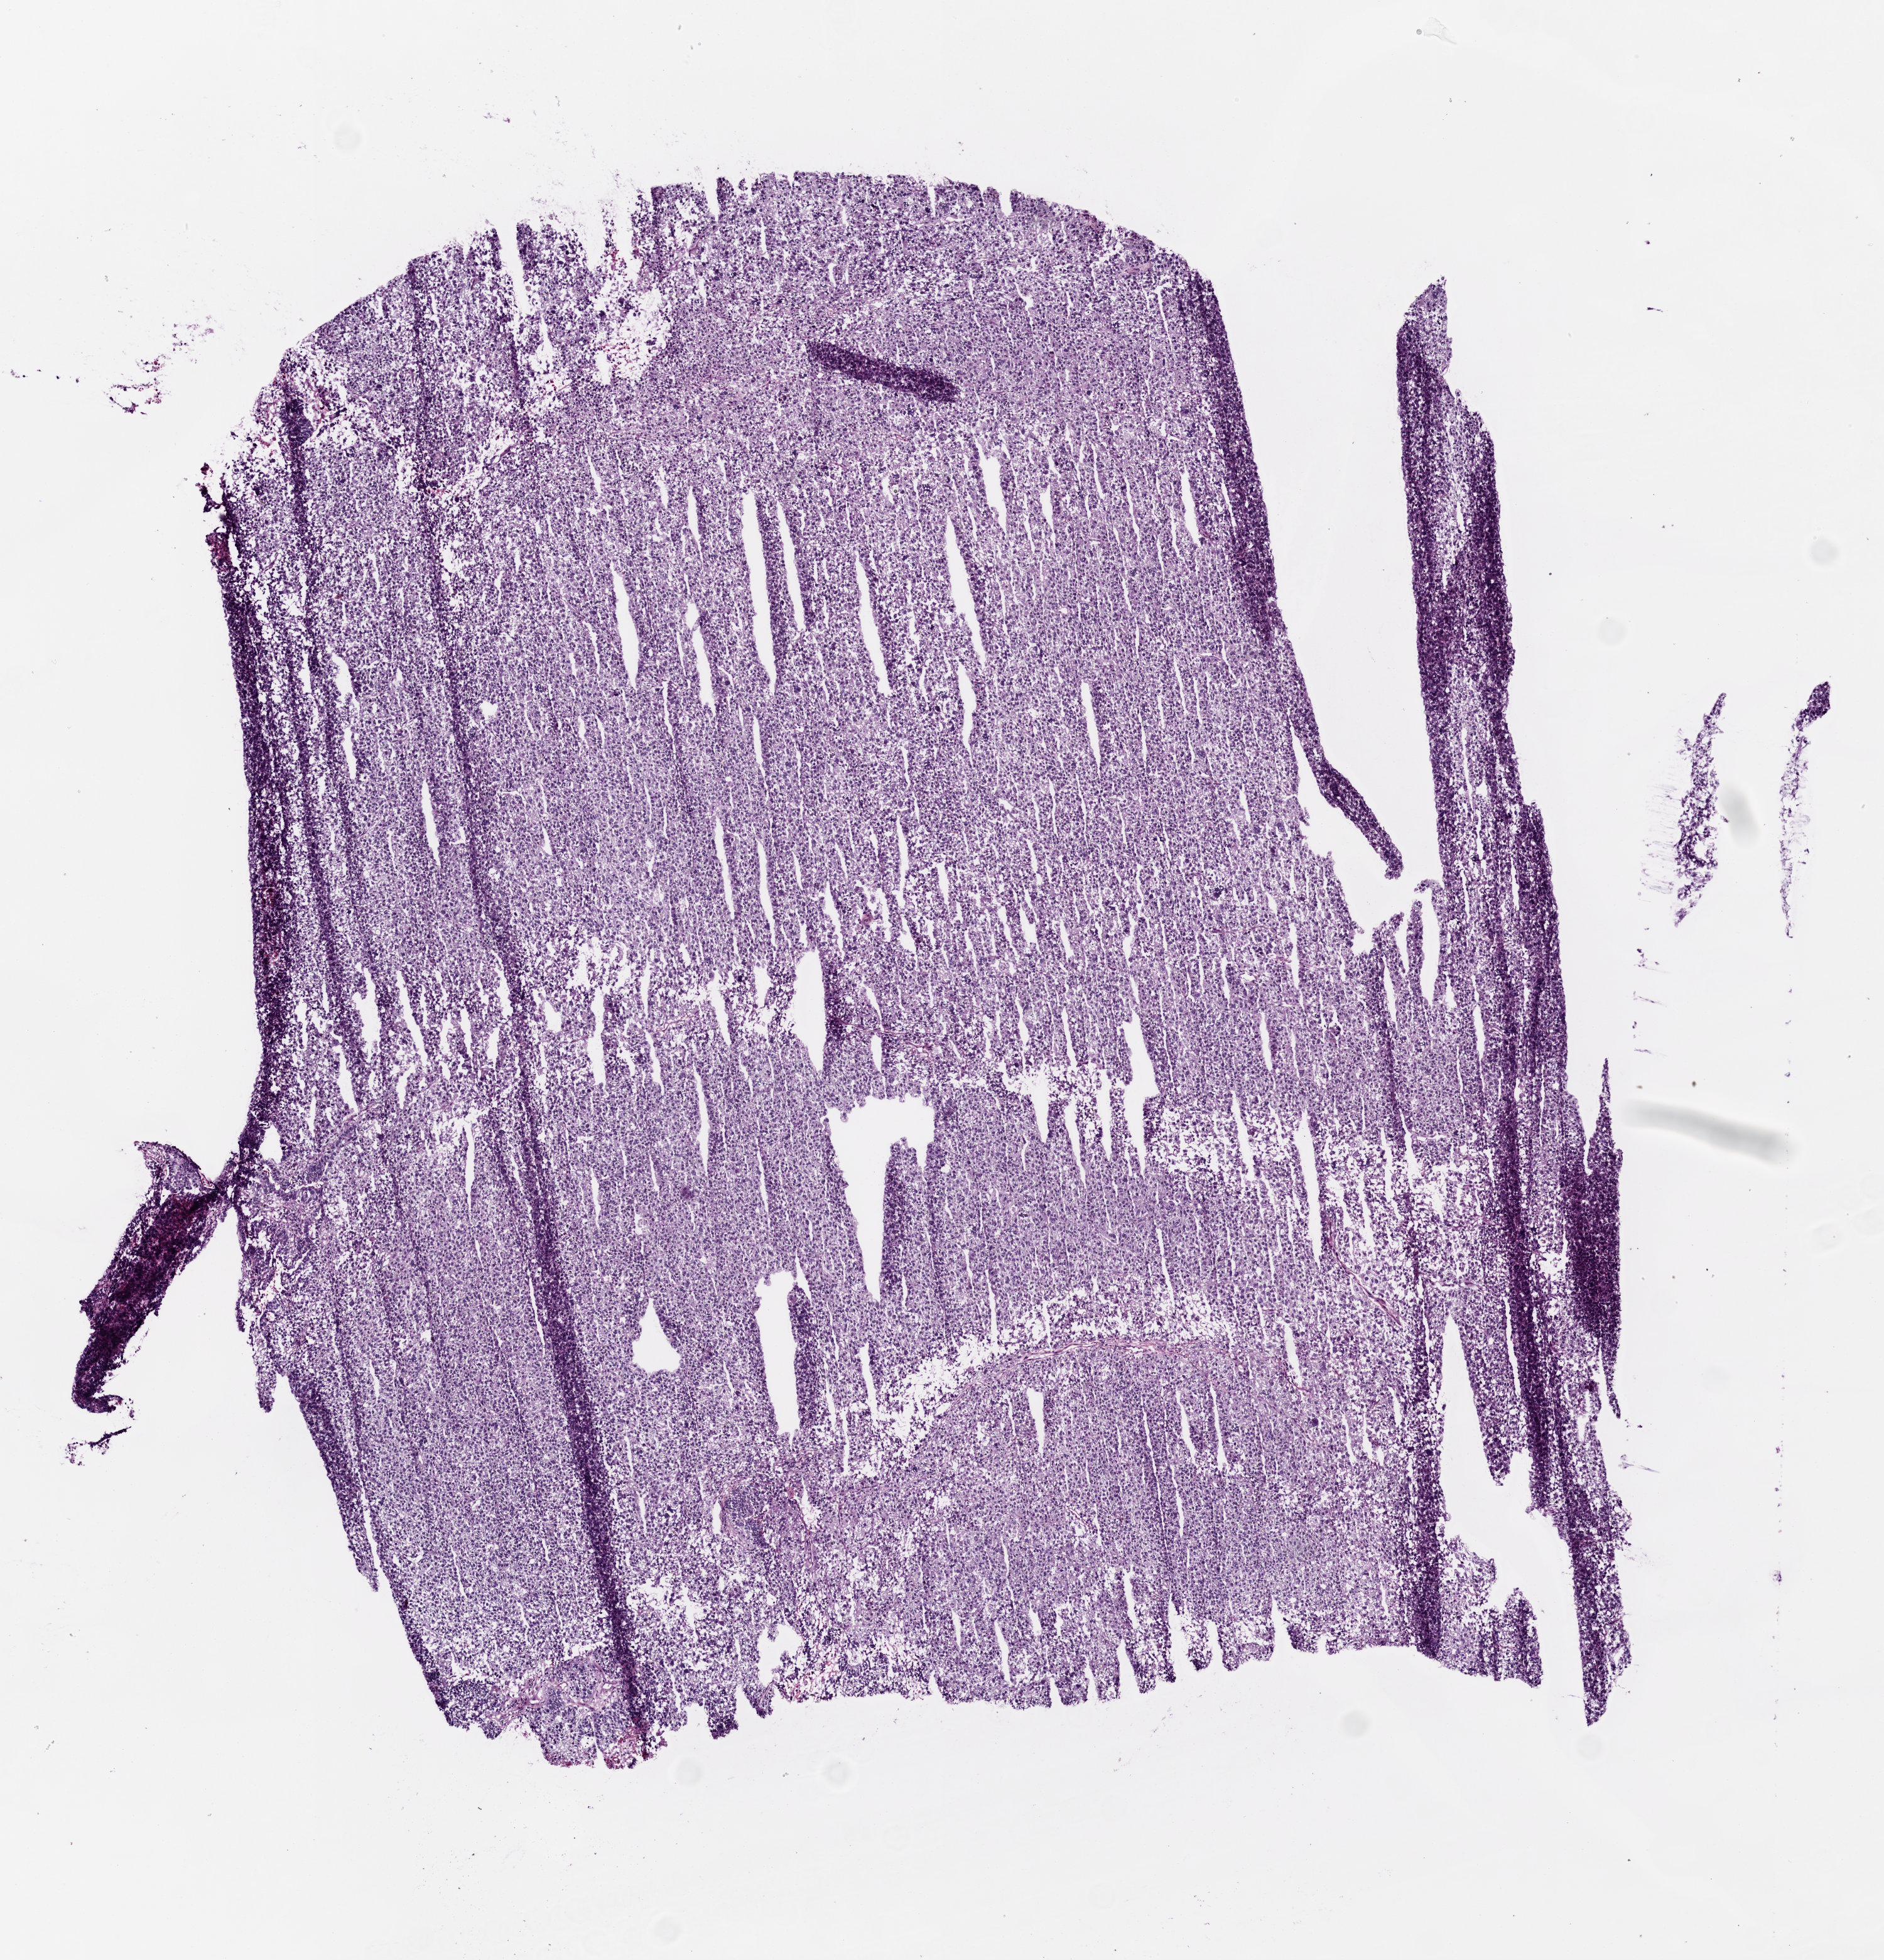
H&E-stained whole-slide image — low-resolution overview of the scanned area, about 6.0 x 6.3 mm; frozen section from the top of the tissue portion; lung, primary tumour sample. Male patient; age at initial diagnosis 65 years. Composition of this section per pathologist review: tumour nuclei 75%, normal cells 0%, stromal cells 5%, necrosis 5%.
• histologic diagnosis: Adenocarcinoma with mixed subtypes (middle lobe, lung)
• AJCC pathologic stage: IIB (5th edition)
• laterality: right